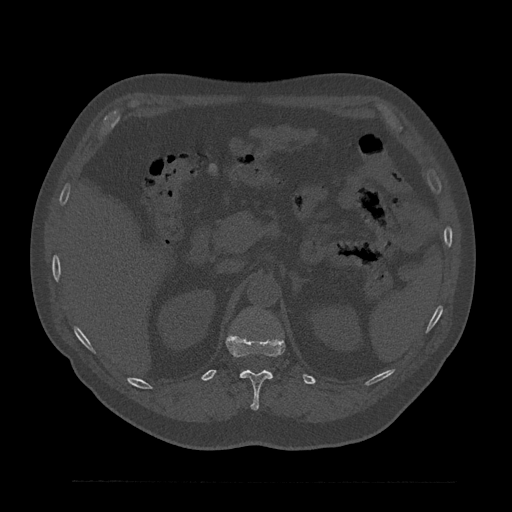
CT including the spine, one axial slice. Slice 215 of 797 in the series (ordered by position). Reconstruction kernel Br40s/3. 120 kVp. Bone window (W 1800 / L 400 HU). 512 × 512 image matrix, field of view 430 × 430 mm. Male patient, age 61 years. From the clinical record (not read from this slice): primary cancer: prostate.
Structures marked on this image (semi-automatically segmented with operator editing):
- T12 vertebra: bounding box <226,333,285,410> (left, top, right, bottom; pixels)